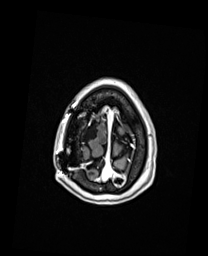
Brain MRI from a brain-tumour surgery series, one axial slice; slice 28 of 192 in the series (ordered by position); T1-weighted post-contrast; 208 × 256 image matrix, field of view 208 × 256 mm. Case-level facts recorded for this patient, not image findings: histopathology: Oligodendroglioma; WHO grade: 3; IDH mutation: yes; tumour location: Right Frontal.
Structures marked on this image (expert manual segmentation):
- previous resection cavity: bounding box <72,120,99,142> (left, top, right, bottom; pixels)